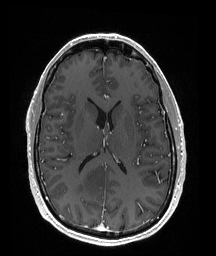
Brain MRI from a brain-tumour surgery series, one axial slice; position 83 of 176 along the scan axis; T1-weighted post-contrast; 1 mm slice thickness; 216 × 256 image matrix. Case-level facts recorded for this patient, not image findings: histopathology: Oligodendroglioma; WHO grade: 2; IDH mutation: yes; tumour location: Right Parietal.
Structures marked on this image (manually delineated by an expert):
- tumour: bounding box [x1, y1, x2, y2] px = [70, 164, 111, 197]